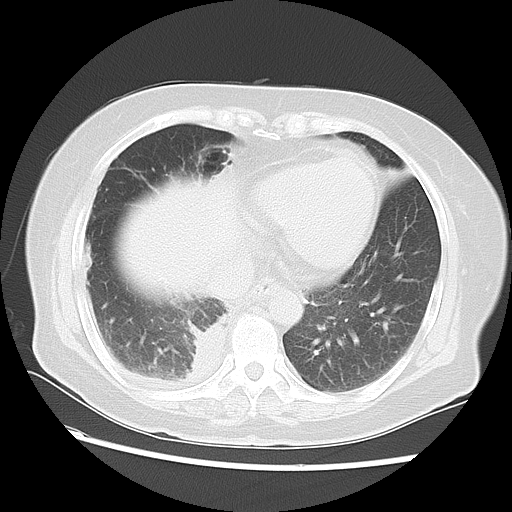
Chest CT, one axial slice. Position 21 of 57 along the scan axis. Lung window (W 1500 / L -600 HU). 5 mm slice thickness. 512 × 512 image matrix, field of view 350 × 350 mm. Female patient, age 69 years. From the clinical record (not read from this slice): clinical TNM (as recorded): T2 N1 M1a.
Annotated regions visible in this slice (rectangle marked by the reading radiologist):
- lung tumour (recorded histology: adenocarcinoma): box from (x=180, y=315) to (x=226, y=389) px